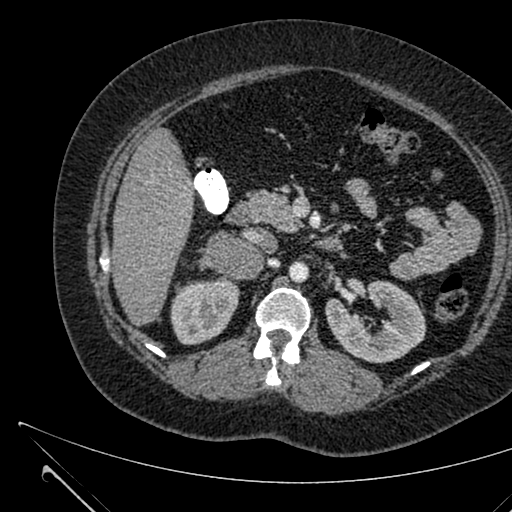
Contrast-enhanced abdominal CT, one axial slice; position 360 of 731 along the scan axis; 120 kVp; intravenous contrast given; soft-tissue window (W 400 / L 40 HU); 1 mm slice thickness; 512 × 512 image matrix. Patient: female, 36 years. From the clinical record (not read from this slice): diagnosis: adrenocortical carcinoma; tumour side: right adrenal; tumour size at pathology: 10 cm; Ki-67 index: 20 %; stage (as recorded): 4.
Annotated regions visible in this slice (semi-automatically segmented with operator editing):
- mass: box from (x=205, y=232) to (x=261, y=278) px